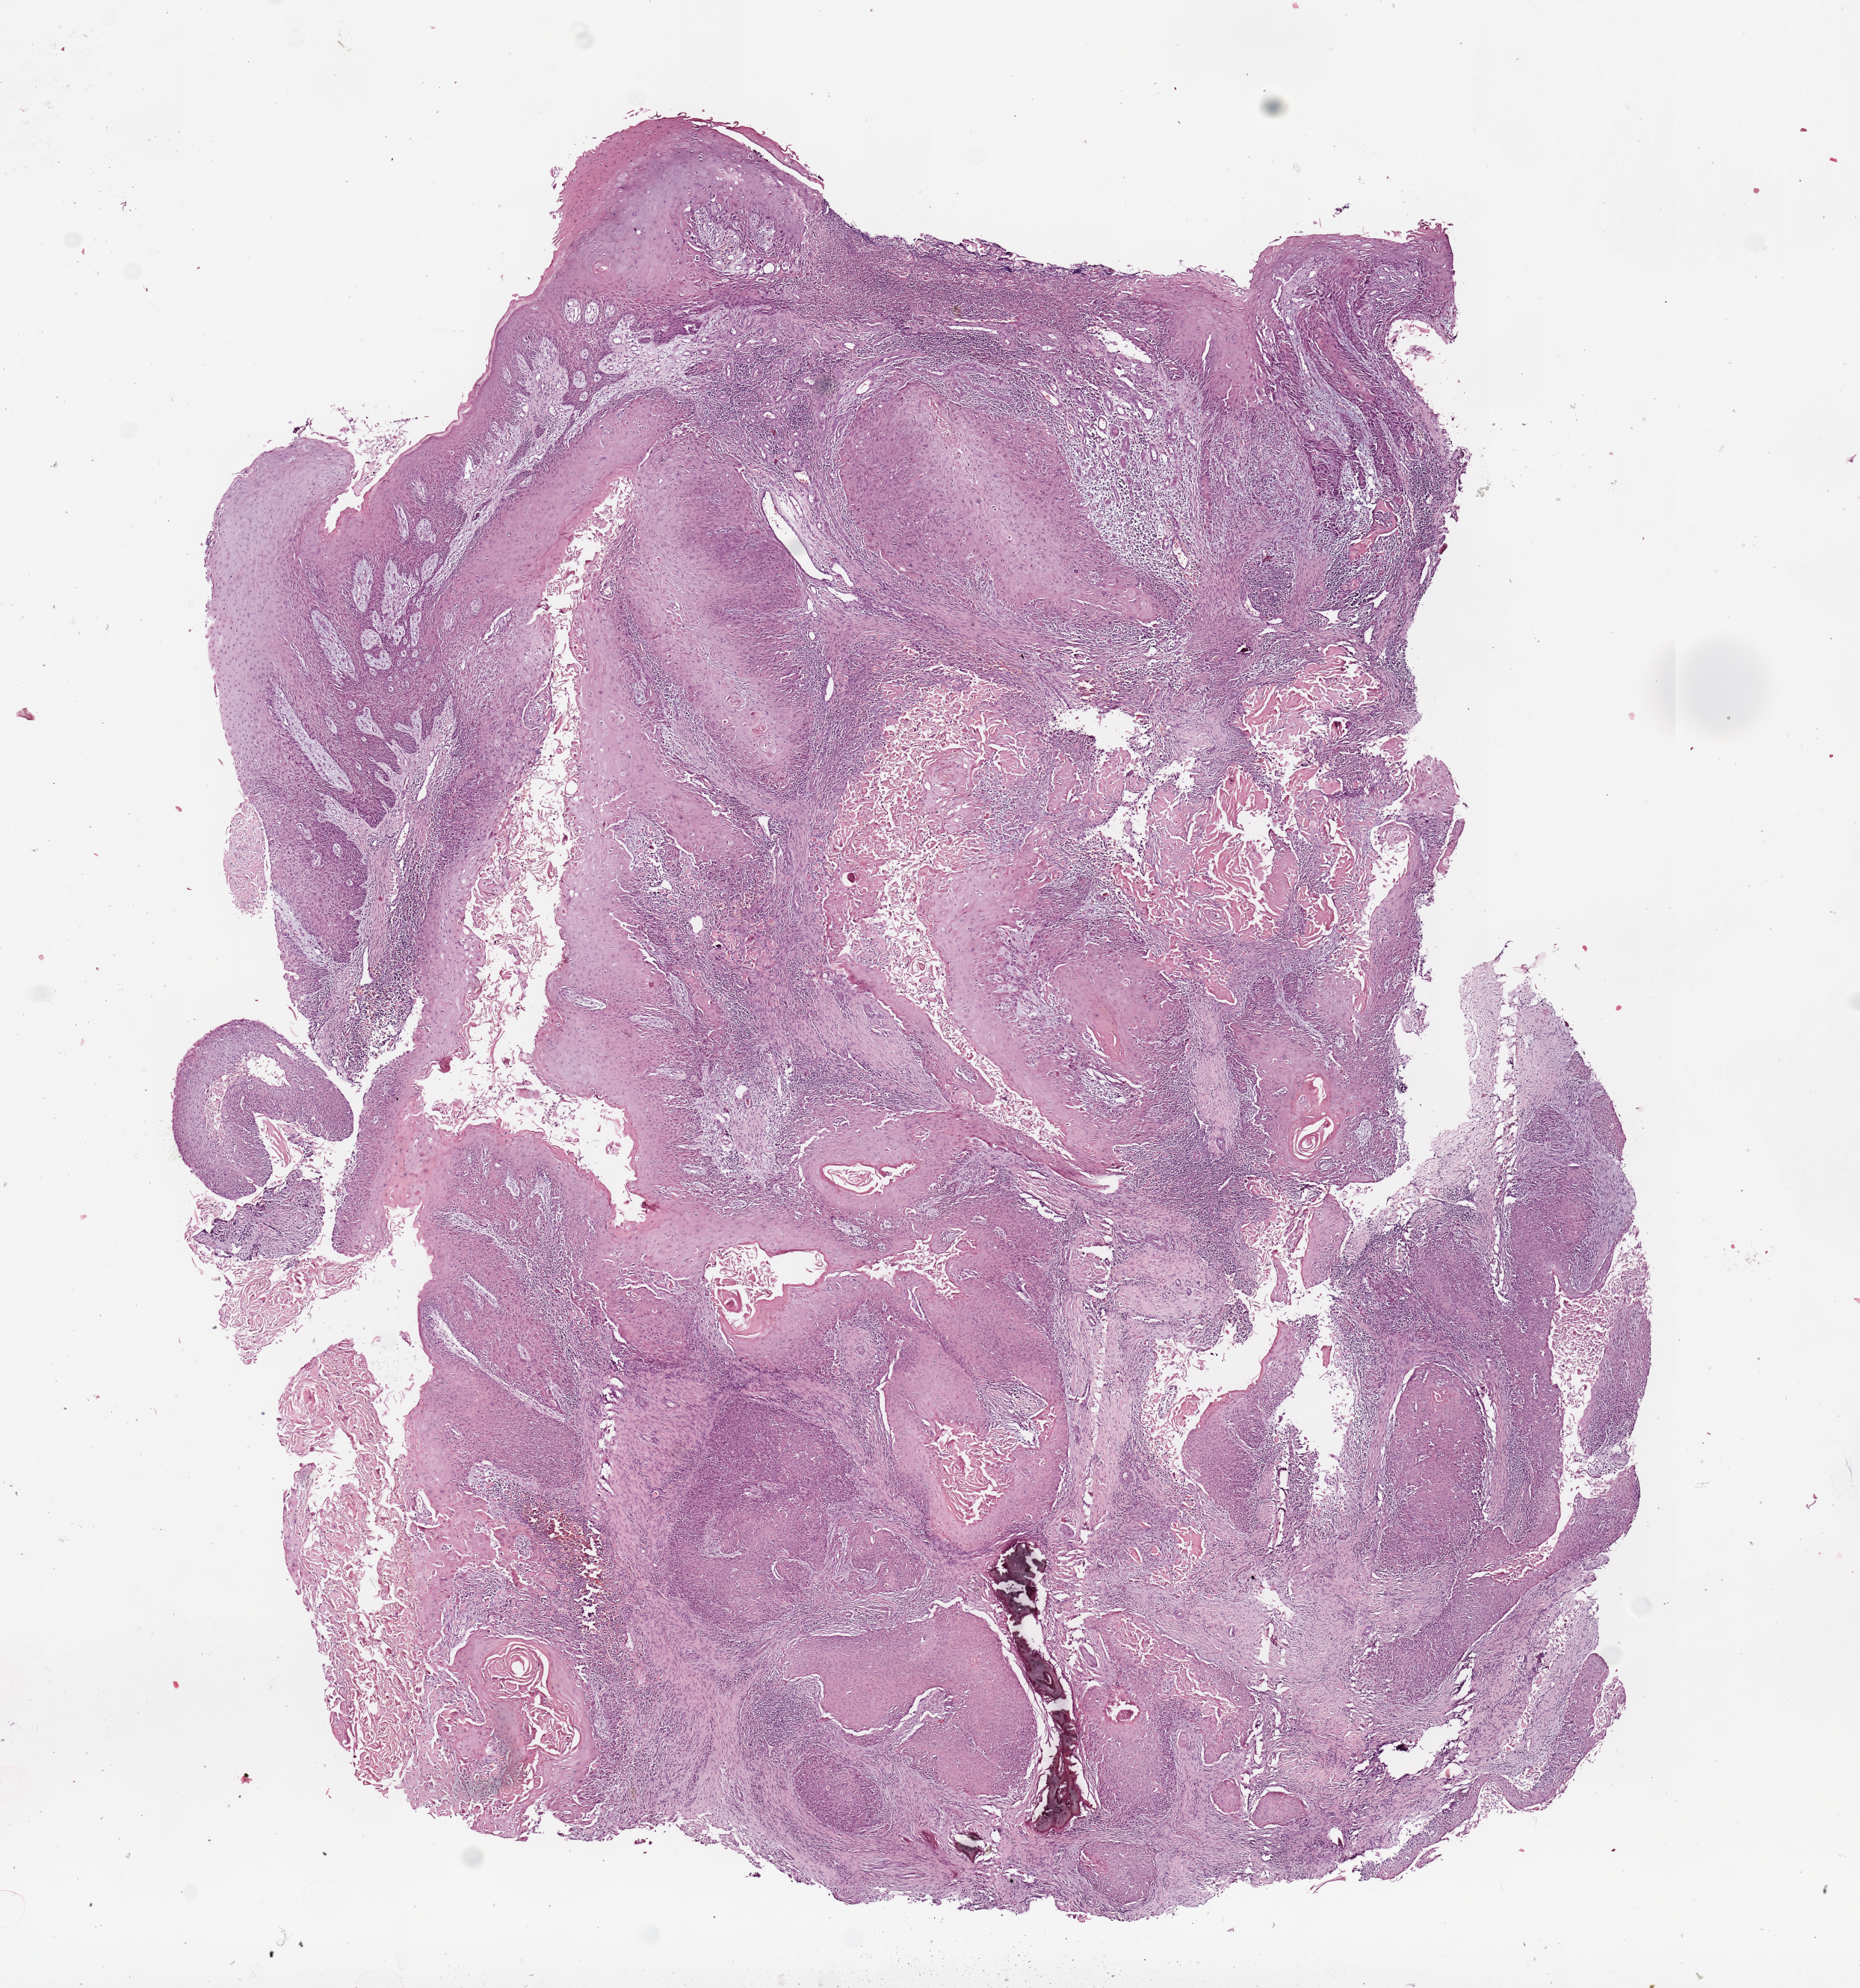
Digitized H&E tissue section (whole slide), a low-resolution overview of the entire scanned area, about 9.8 x 10.5 mm (acquisition: 20x scan); head and neck, tissue type not recorded. Patient: female, age 53 years.
- patient diagnosis: Squamous cell carcinoma, NOS (gum, NOS)